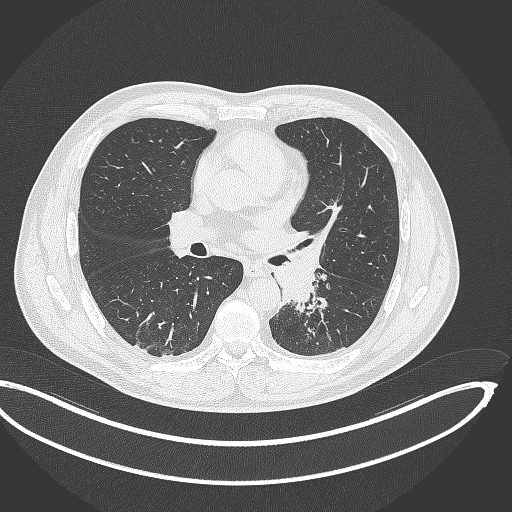
Chest CT, one axial slice. Position 192 of 362 along the scan axis. Reconstruction kernel B70f. 120 kVp. Lung window (W 1500 / L -600 HU). 1 mm slice thickness. 512 × 512 image matrix. Patient: male, 50 years. Case-level facts recorded for this patient, not image findings: clinical TNM (as recorded): T2a N3 M0.
Annotated regions visible in this slice (rectangle marked by the reading radiologist):
- lung tumour (recorded histology: squamous cell carcinoma): bounding box (x1, y1, x2, y2) in pixels: (269, 241, 327, 307)